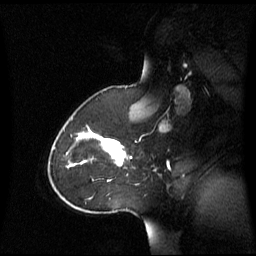
Breast MRI (dynamic contrast-enhanced), one sagittal slice. Position 44 of 60 along the scan axis. Dynamic contrast-enhanced series, image 2 of 3 at this slice position (ordered by acquisition). 1.5 T. TE 4.2 ms, TR 8.4 ms. 256 × 256 image matrix, field of view 270 × 270 mm. Patient: female, 43 years. From the clinical record (not read from this slice): setting: breast cancer imaged before/during neoadjuvant chemotherapy; receptor status: triple-negative.
Outlined on this slice (semi-automatic segmentation, software-assisted and operator-edited):
- analysis volume of interest (the breast-tissue region the enhancement analysis was run in; not a lesion): bounding box (x1, y1, x2, y2) in pixels: (62, 124, 128, 180)
- tumour enhancement mask (voxels above the 70 % enhancement threshold inside the analysis volume of interest): (79, 126, 126, 166)